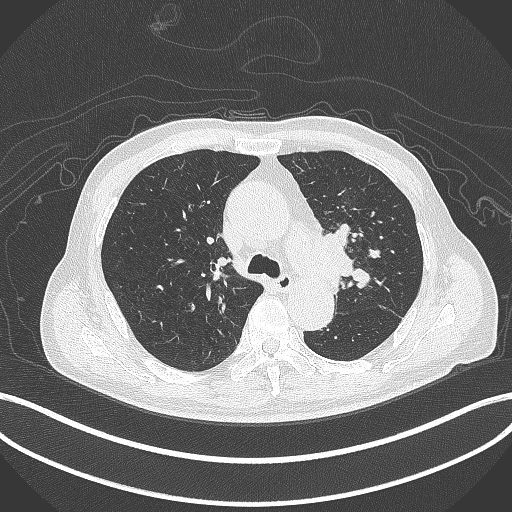
Chest CT, one axial slice; position 293 of 417 along the scan axis; reconstruction kernel B70f; 120 kVp; lung window (W 1500 / L -600 HU); 1 mm slice thickness; 512 × 512 image matrix, field of view 400 × 400 mm. Patient: male, 77 years. From the clinical record (not read from this slice): clinical TNM (as recorded): T3 N1 M0.
Outlined on this slice (rectangle marked by the reading radiologist):
- lung tumour (recorded histology: adenocarcinoma): bounding box [x1, y1, x2, y2] px = [317, 228, 356, 289]